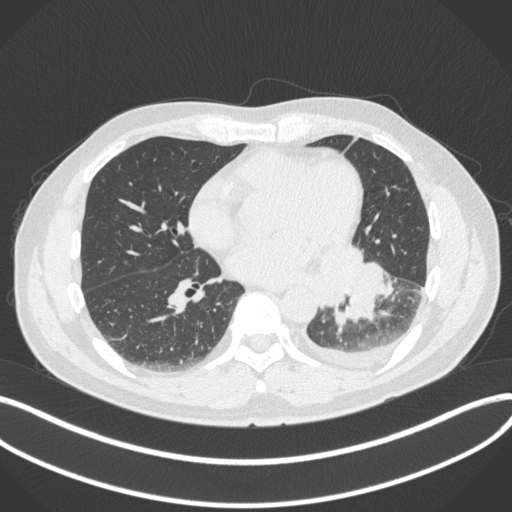
Chest CT, one axial slice; position 156 of 350 along the scan axis; lung window (W 1500 / L -600 HU); 1 mm slice thickness; 512 × 512 image matrix, field of view 400 × 400 mm. Male patient, age 58 years. Case-level facts recorded for this patient, not image findings: clinical TNM (as recorded): T3 N1 M1b; histopathological grade: G3.
Annotated regions visible in this slice (bounding box drawn by a radiologist):
- lung tumour (recorded histology: small cell carcinoma): bounding box <326,247,388,331> (left, top, right, bottom; pixels)